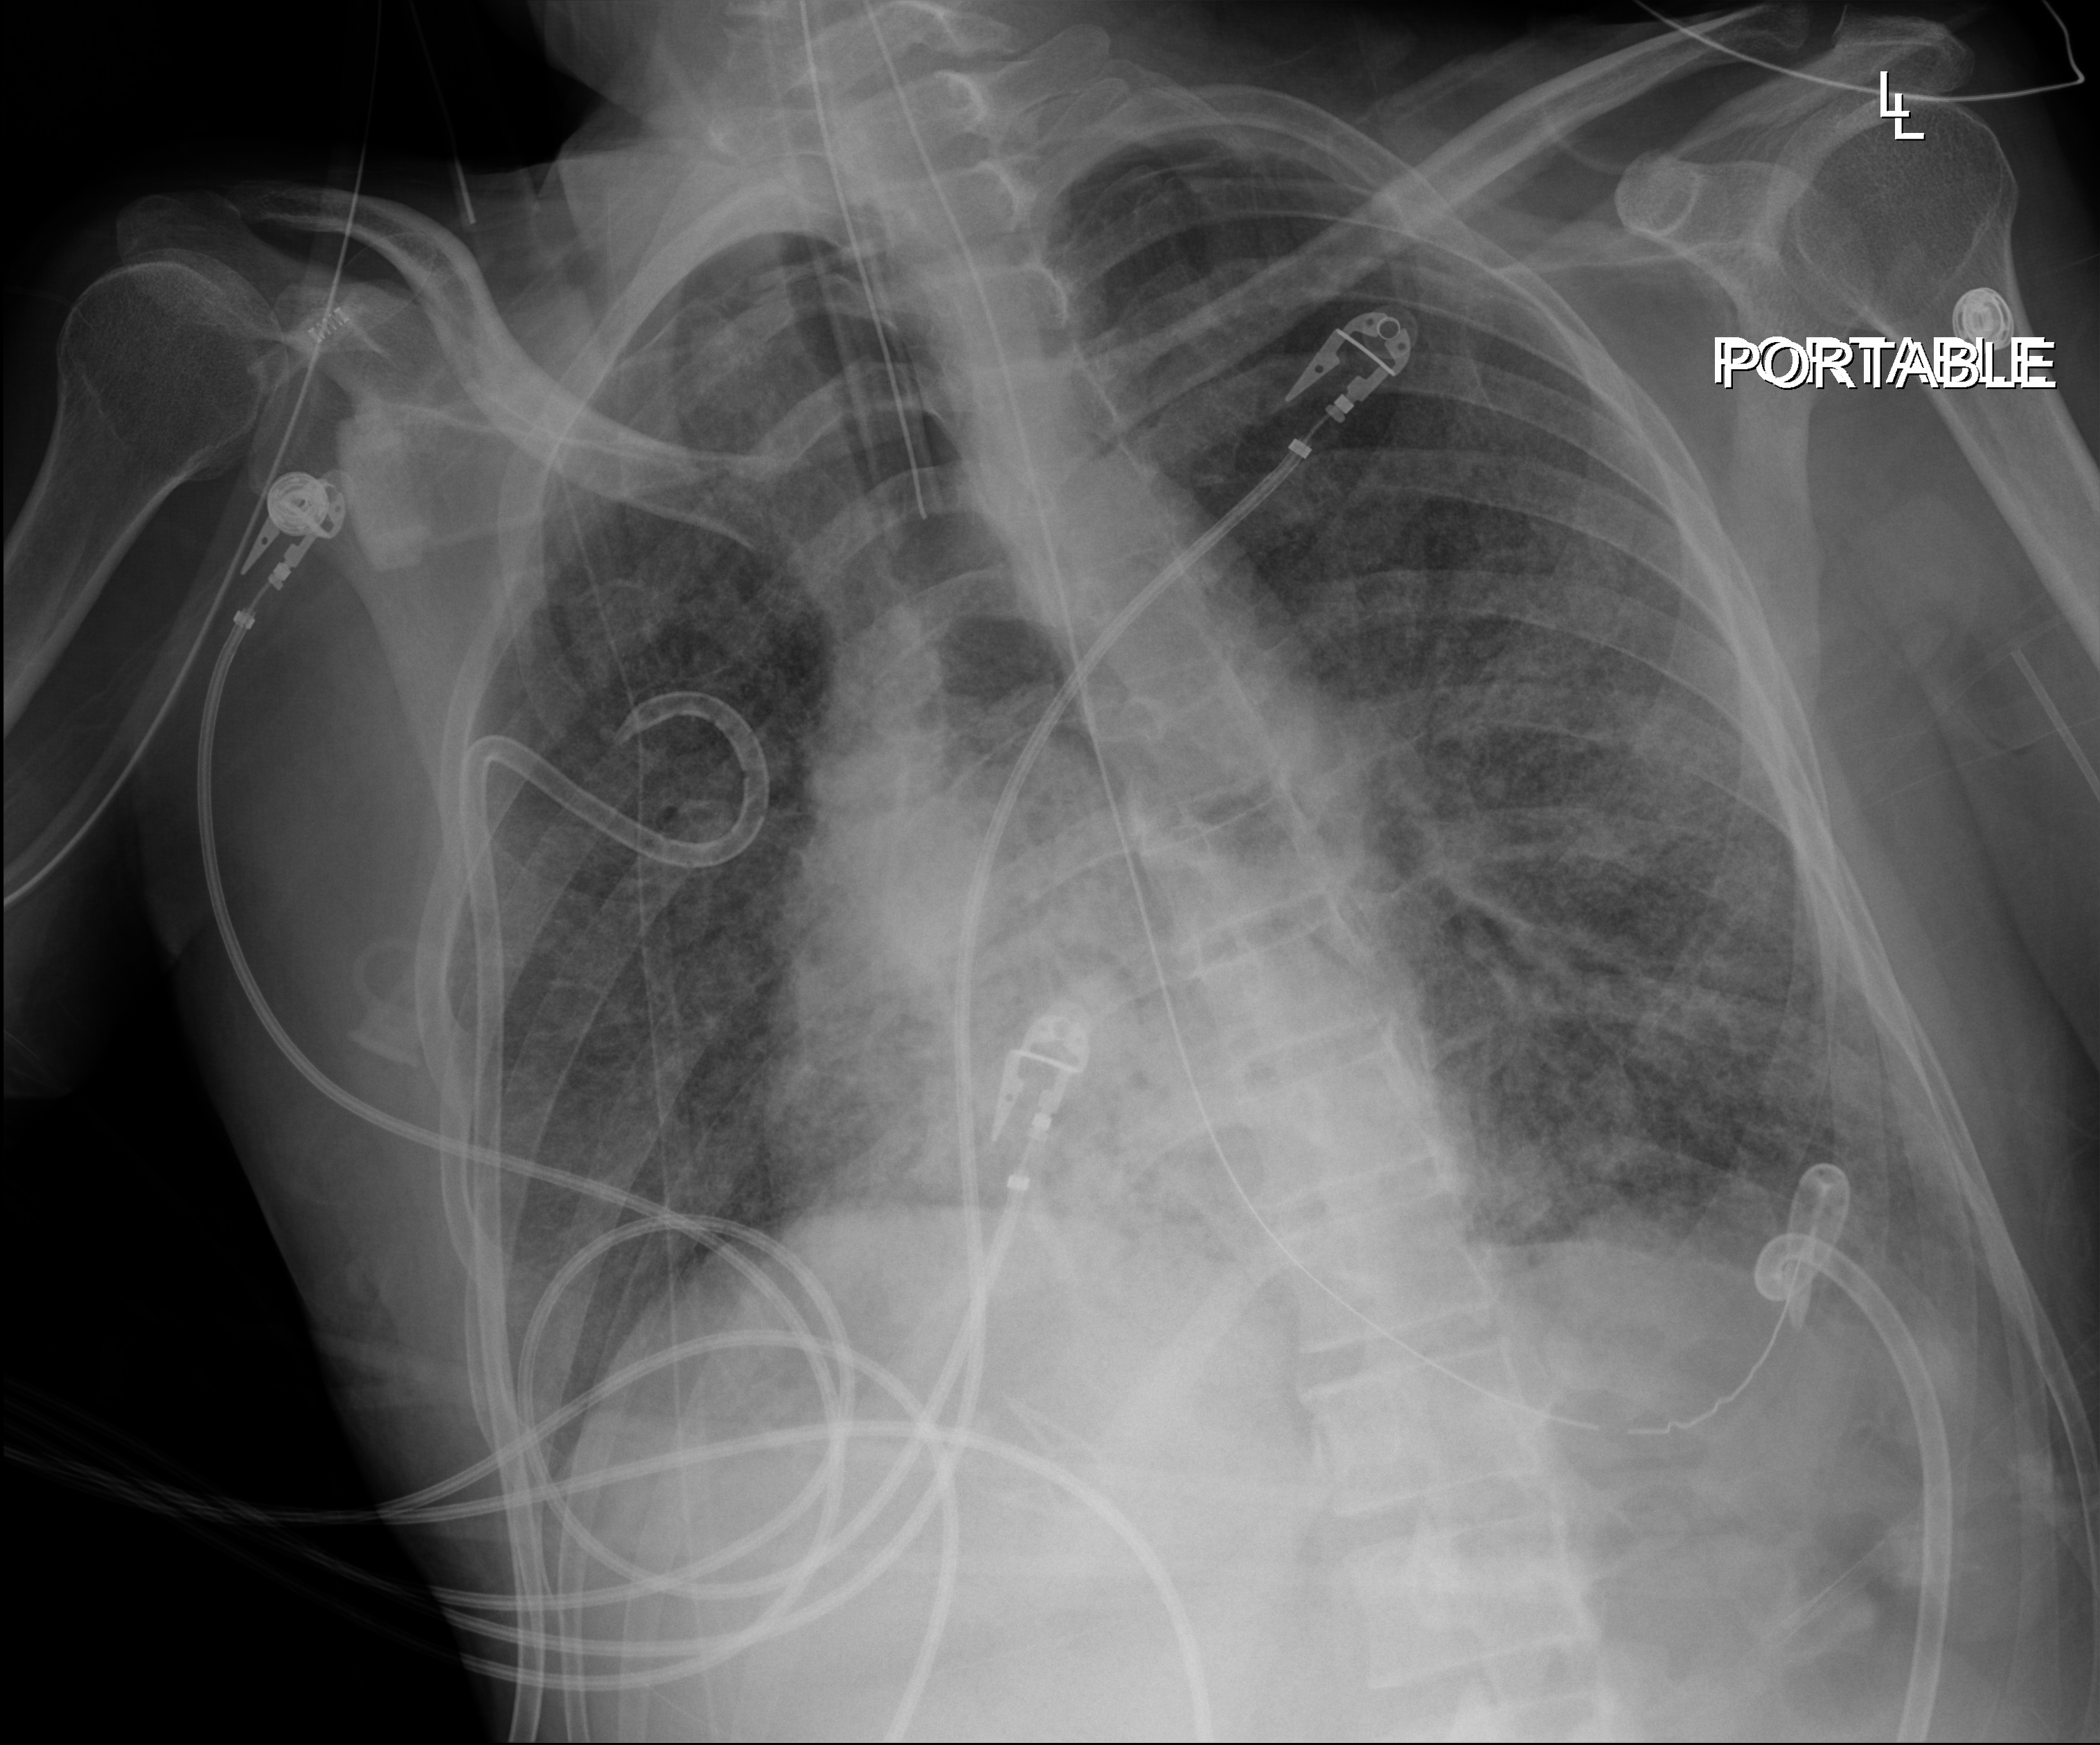
Portable chest radiograph; anteroposterior (AP) projection. Adult patient hospitalised with COVID-19, age 18–59 years.
From the hospital-stay record, not from the radiograph (when in the stay this image was taken is not recorded): chronic kidney disease (admission record): no.